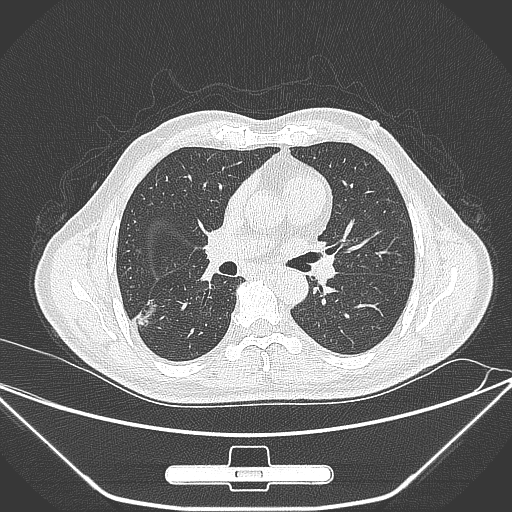
Chest CT, one axial slice; slice 156 of 309 in the series (ordered by position); 120 kVp; lung window (W 1500 / L -600 HU); 512 × 512 image matrix. Patient: male, 71 years. From the clinical record (not read from this slice): clinical TNM (as recorded): T1c N0 M0; histopathological grade: G2.
Outlined on this slice (rectangle marked by the reading radiologist):
- lung tumour (recorded histology: adenocarcinoma): bounding box <131,298,166,328> (left, top, right, bottom; pixels)